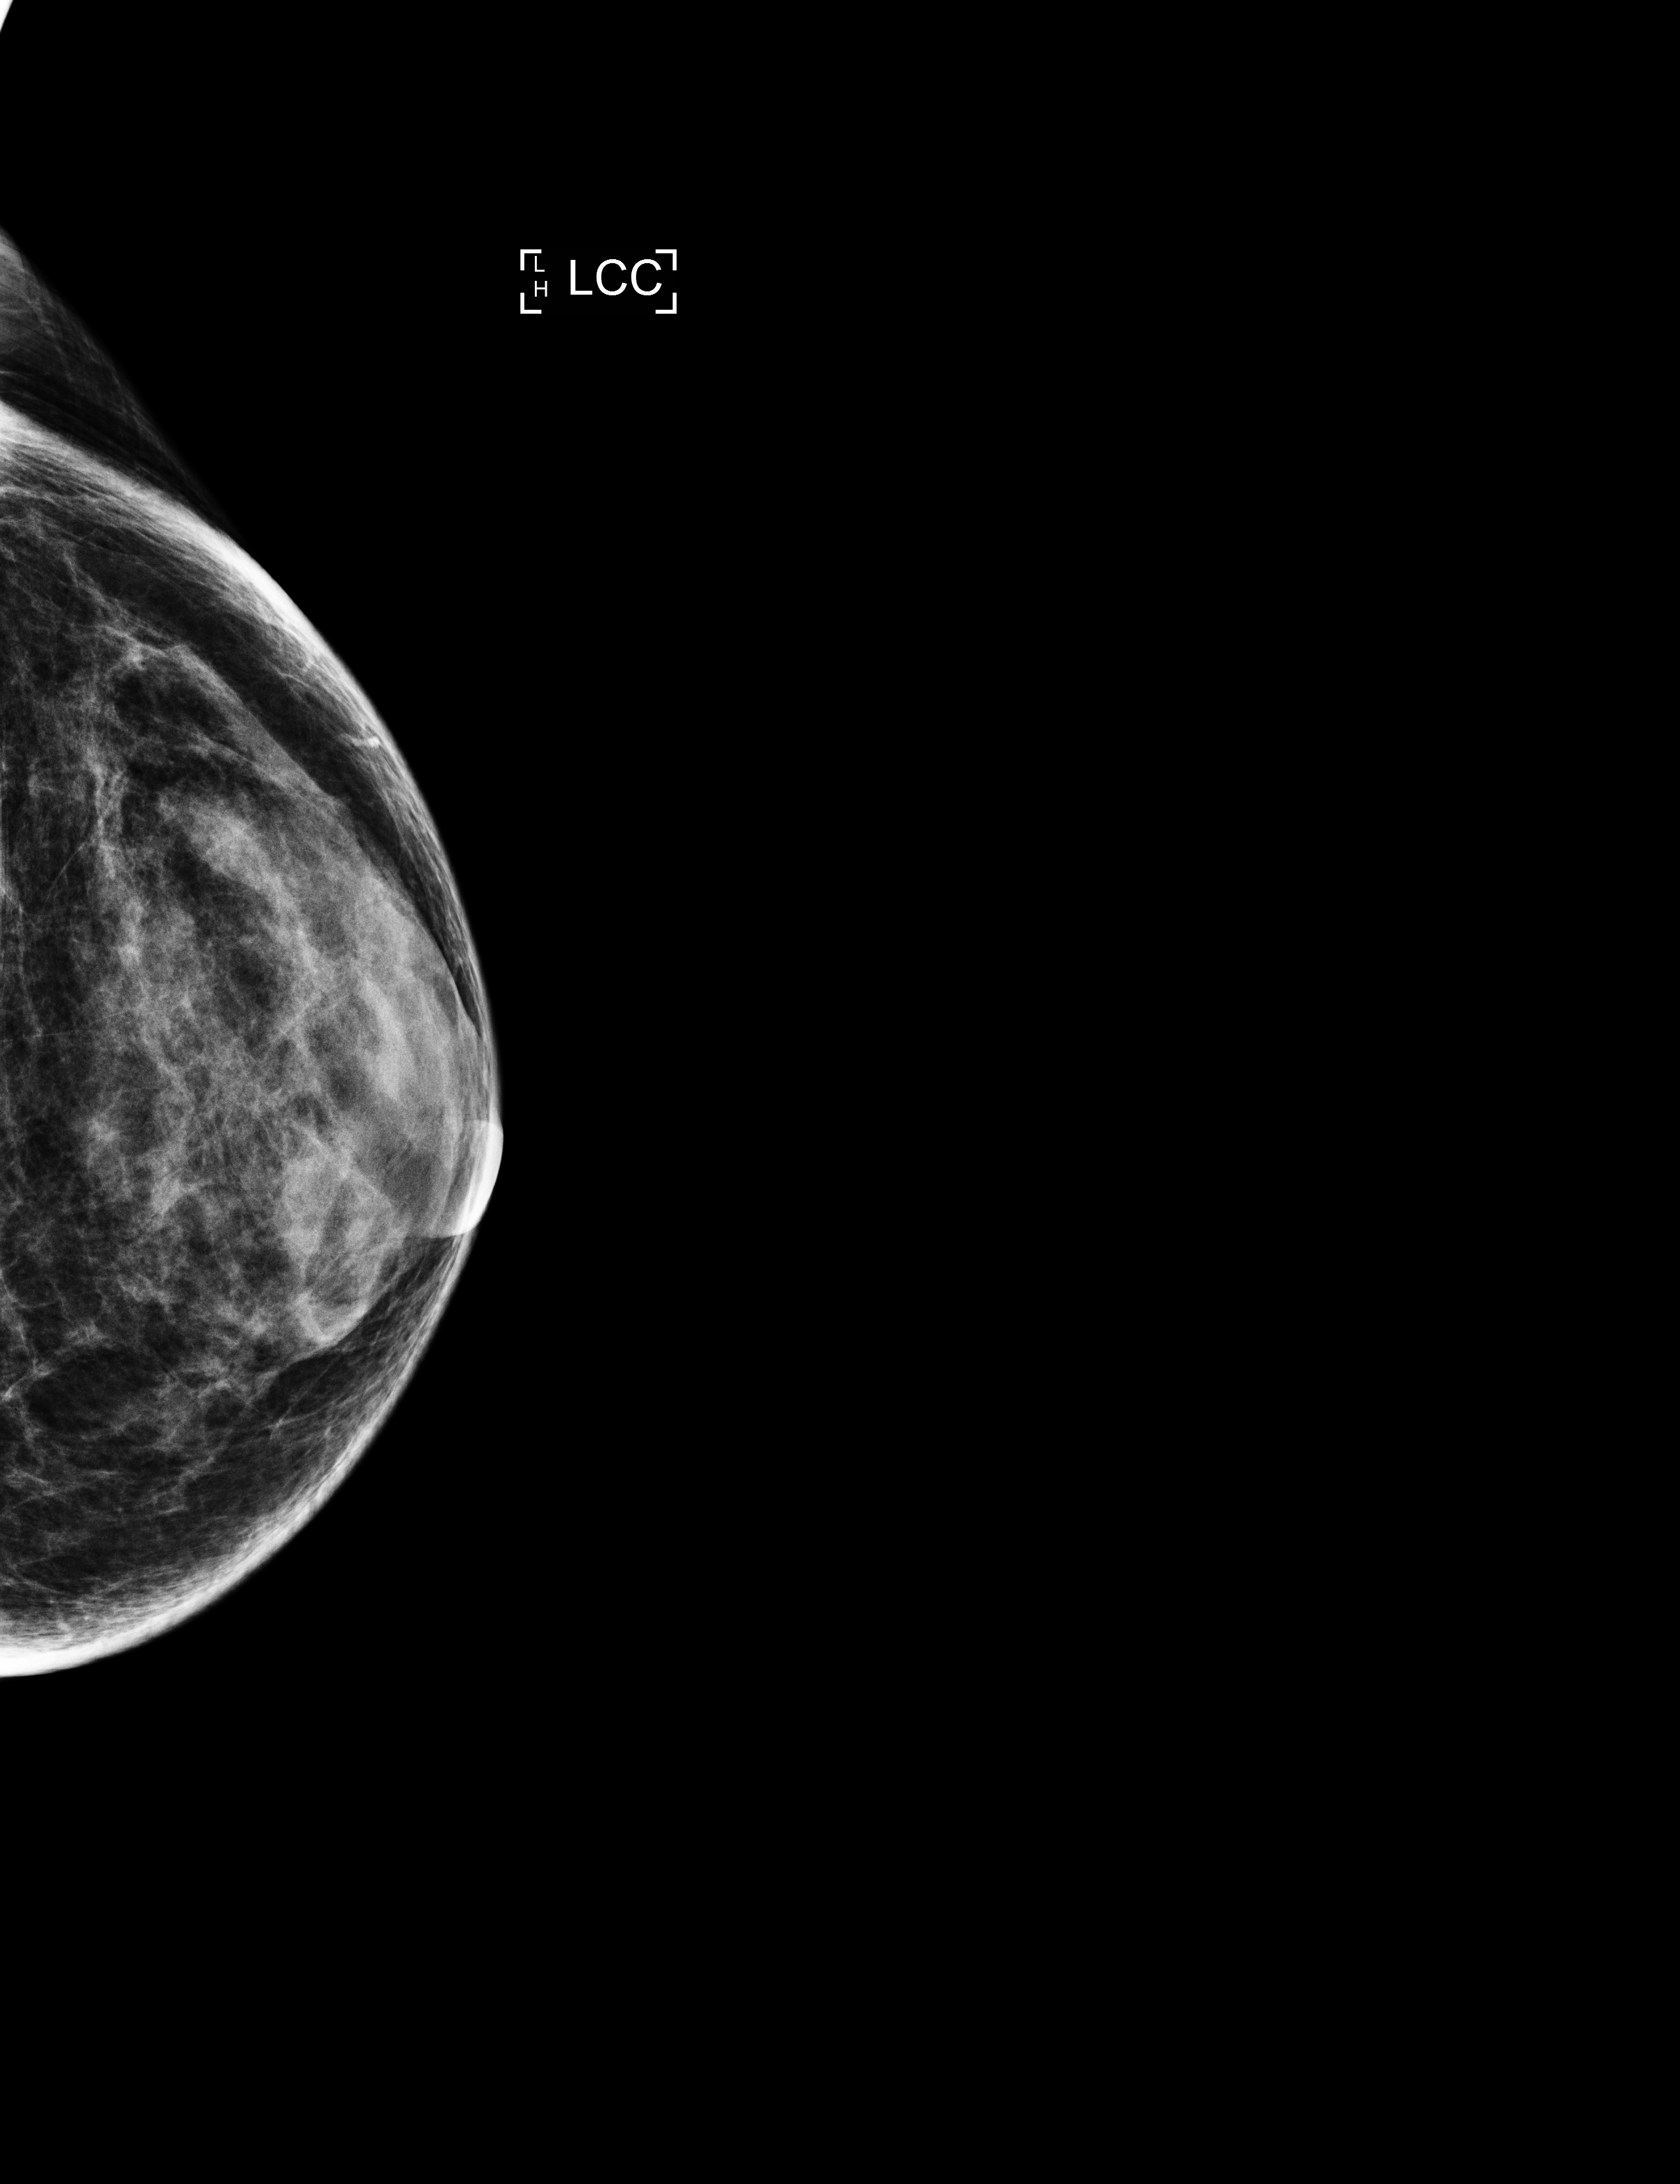
Screening examination. Patient: female, 67 years.
Image type: full-field digital mammogram. Breast: left. Projection: CC view.